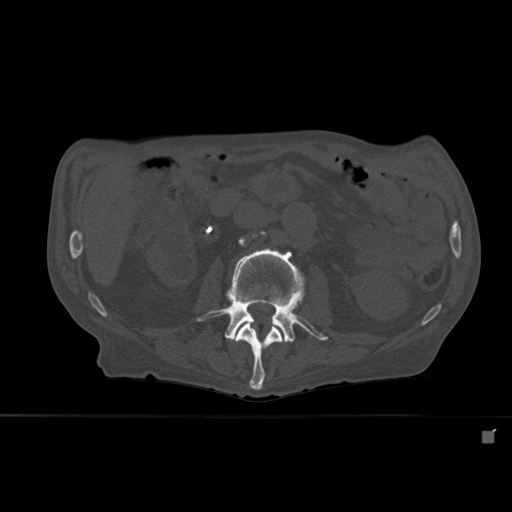
CT including the spine, one axial slice; position 221 of 527 along the scan axis; bone window (W 1800 / L 400 HU); 1.5 mm slice thickness; 512 × 512 image matrix, field of view 373 × 373 mm. Patient: male, 78 years. From the clinical record (not read from this slice): primary cancer: prostate.
Outlined on this slice (semi-automatically segmented with operator editing):
- L2 vertebra: bounding box (x1, y1, x2, y2) in pixels: (234, 323, 283, 390)
- L3 vertebra: (197, 238, 328, 342)